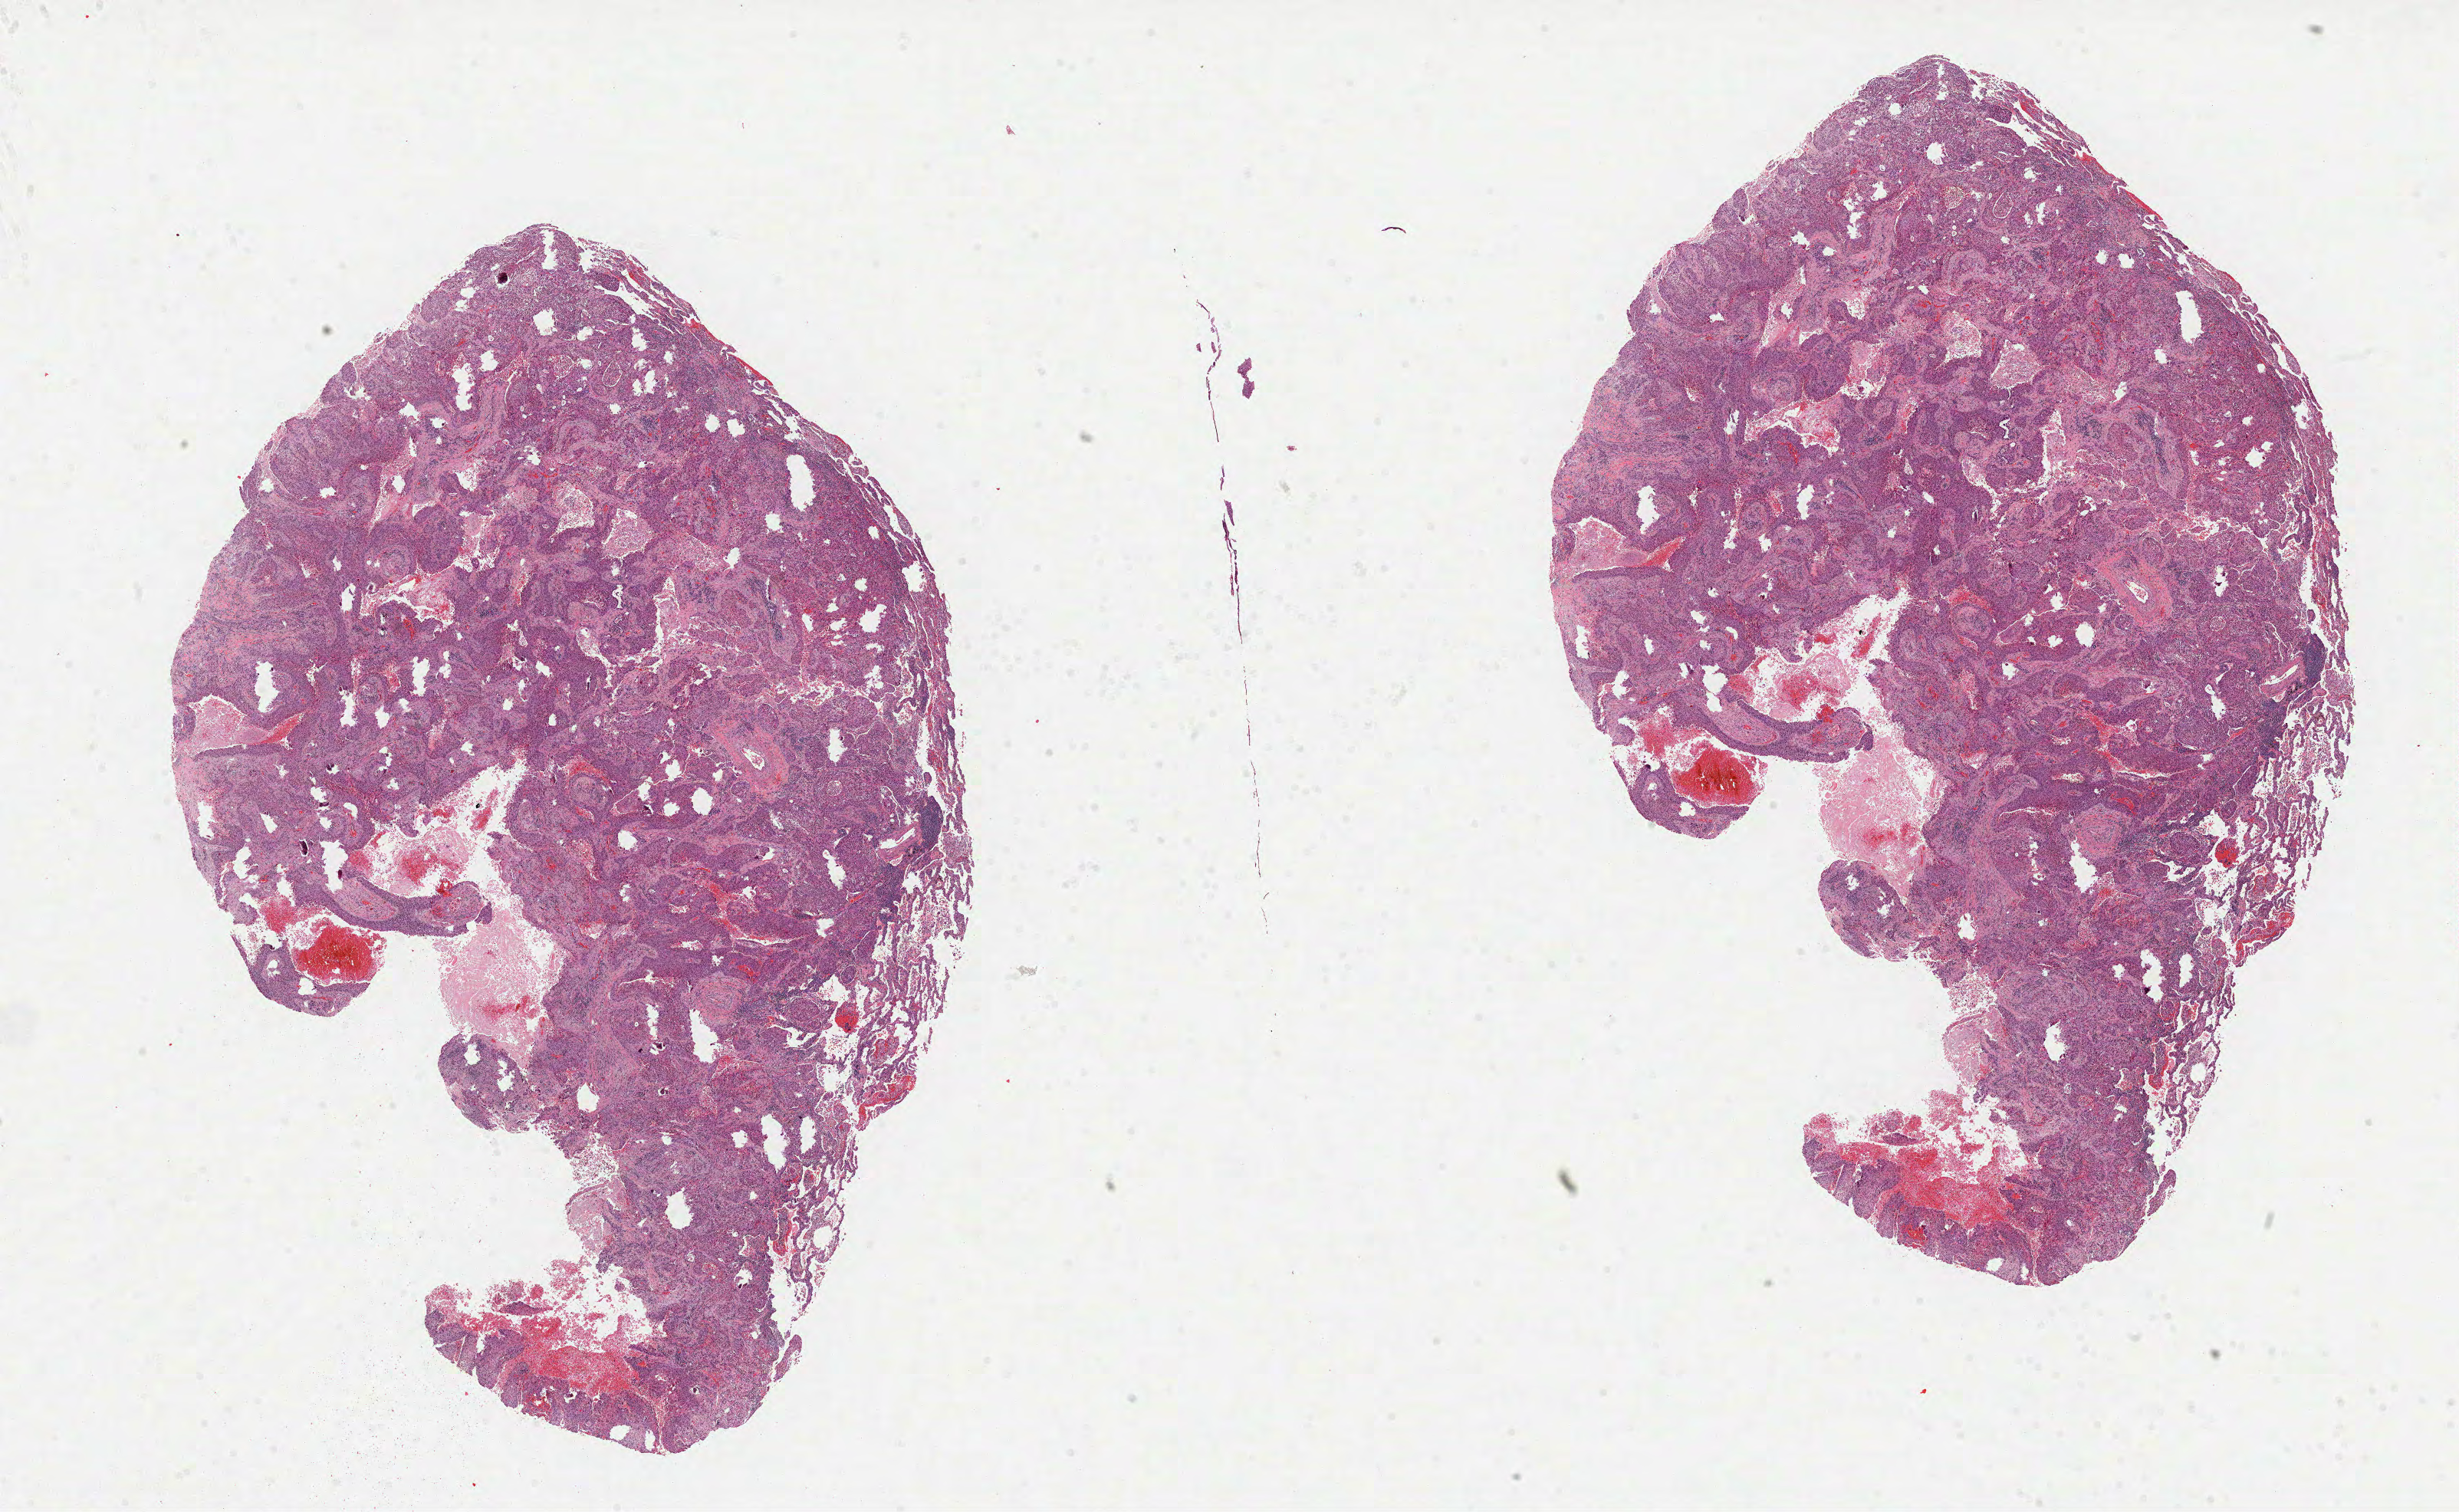
Digitized H&E-stained tissue section (whole slide), a low-resolution overview of the entire scanned area, about 25.9 x 15.9 mm (from a 40x scan), FFPE section, sample: primary tumour, lung. Female, age 73 years at initial diagnosis.
AJCC pathologic stage: IB (6th edition). Diagnosis: Squamous cell carcinoma, NOS.